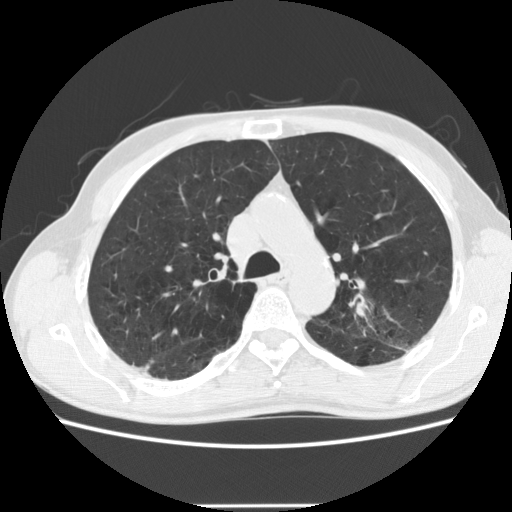
Low-dose screening chest CT, one axial slice; position 137 of 191 along the scan axis; reconstruction kernel STANDARD; 120 kVp; lung window (W 1500 / L -600 HU); 2.5 mm slice thickness; 512 × 512 image matrix, field of view 352 × 352 mm.
Annotated regions visible in this slice (outlined manually by an expert reader):
- lesion 1 (tumor, upper lobe of left lung): bounding box [x1, y1, x2, y2] px = [356, 301, 368, 317]